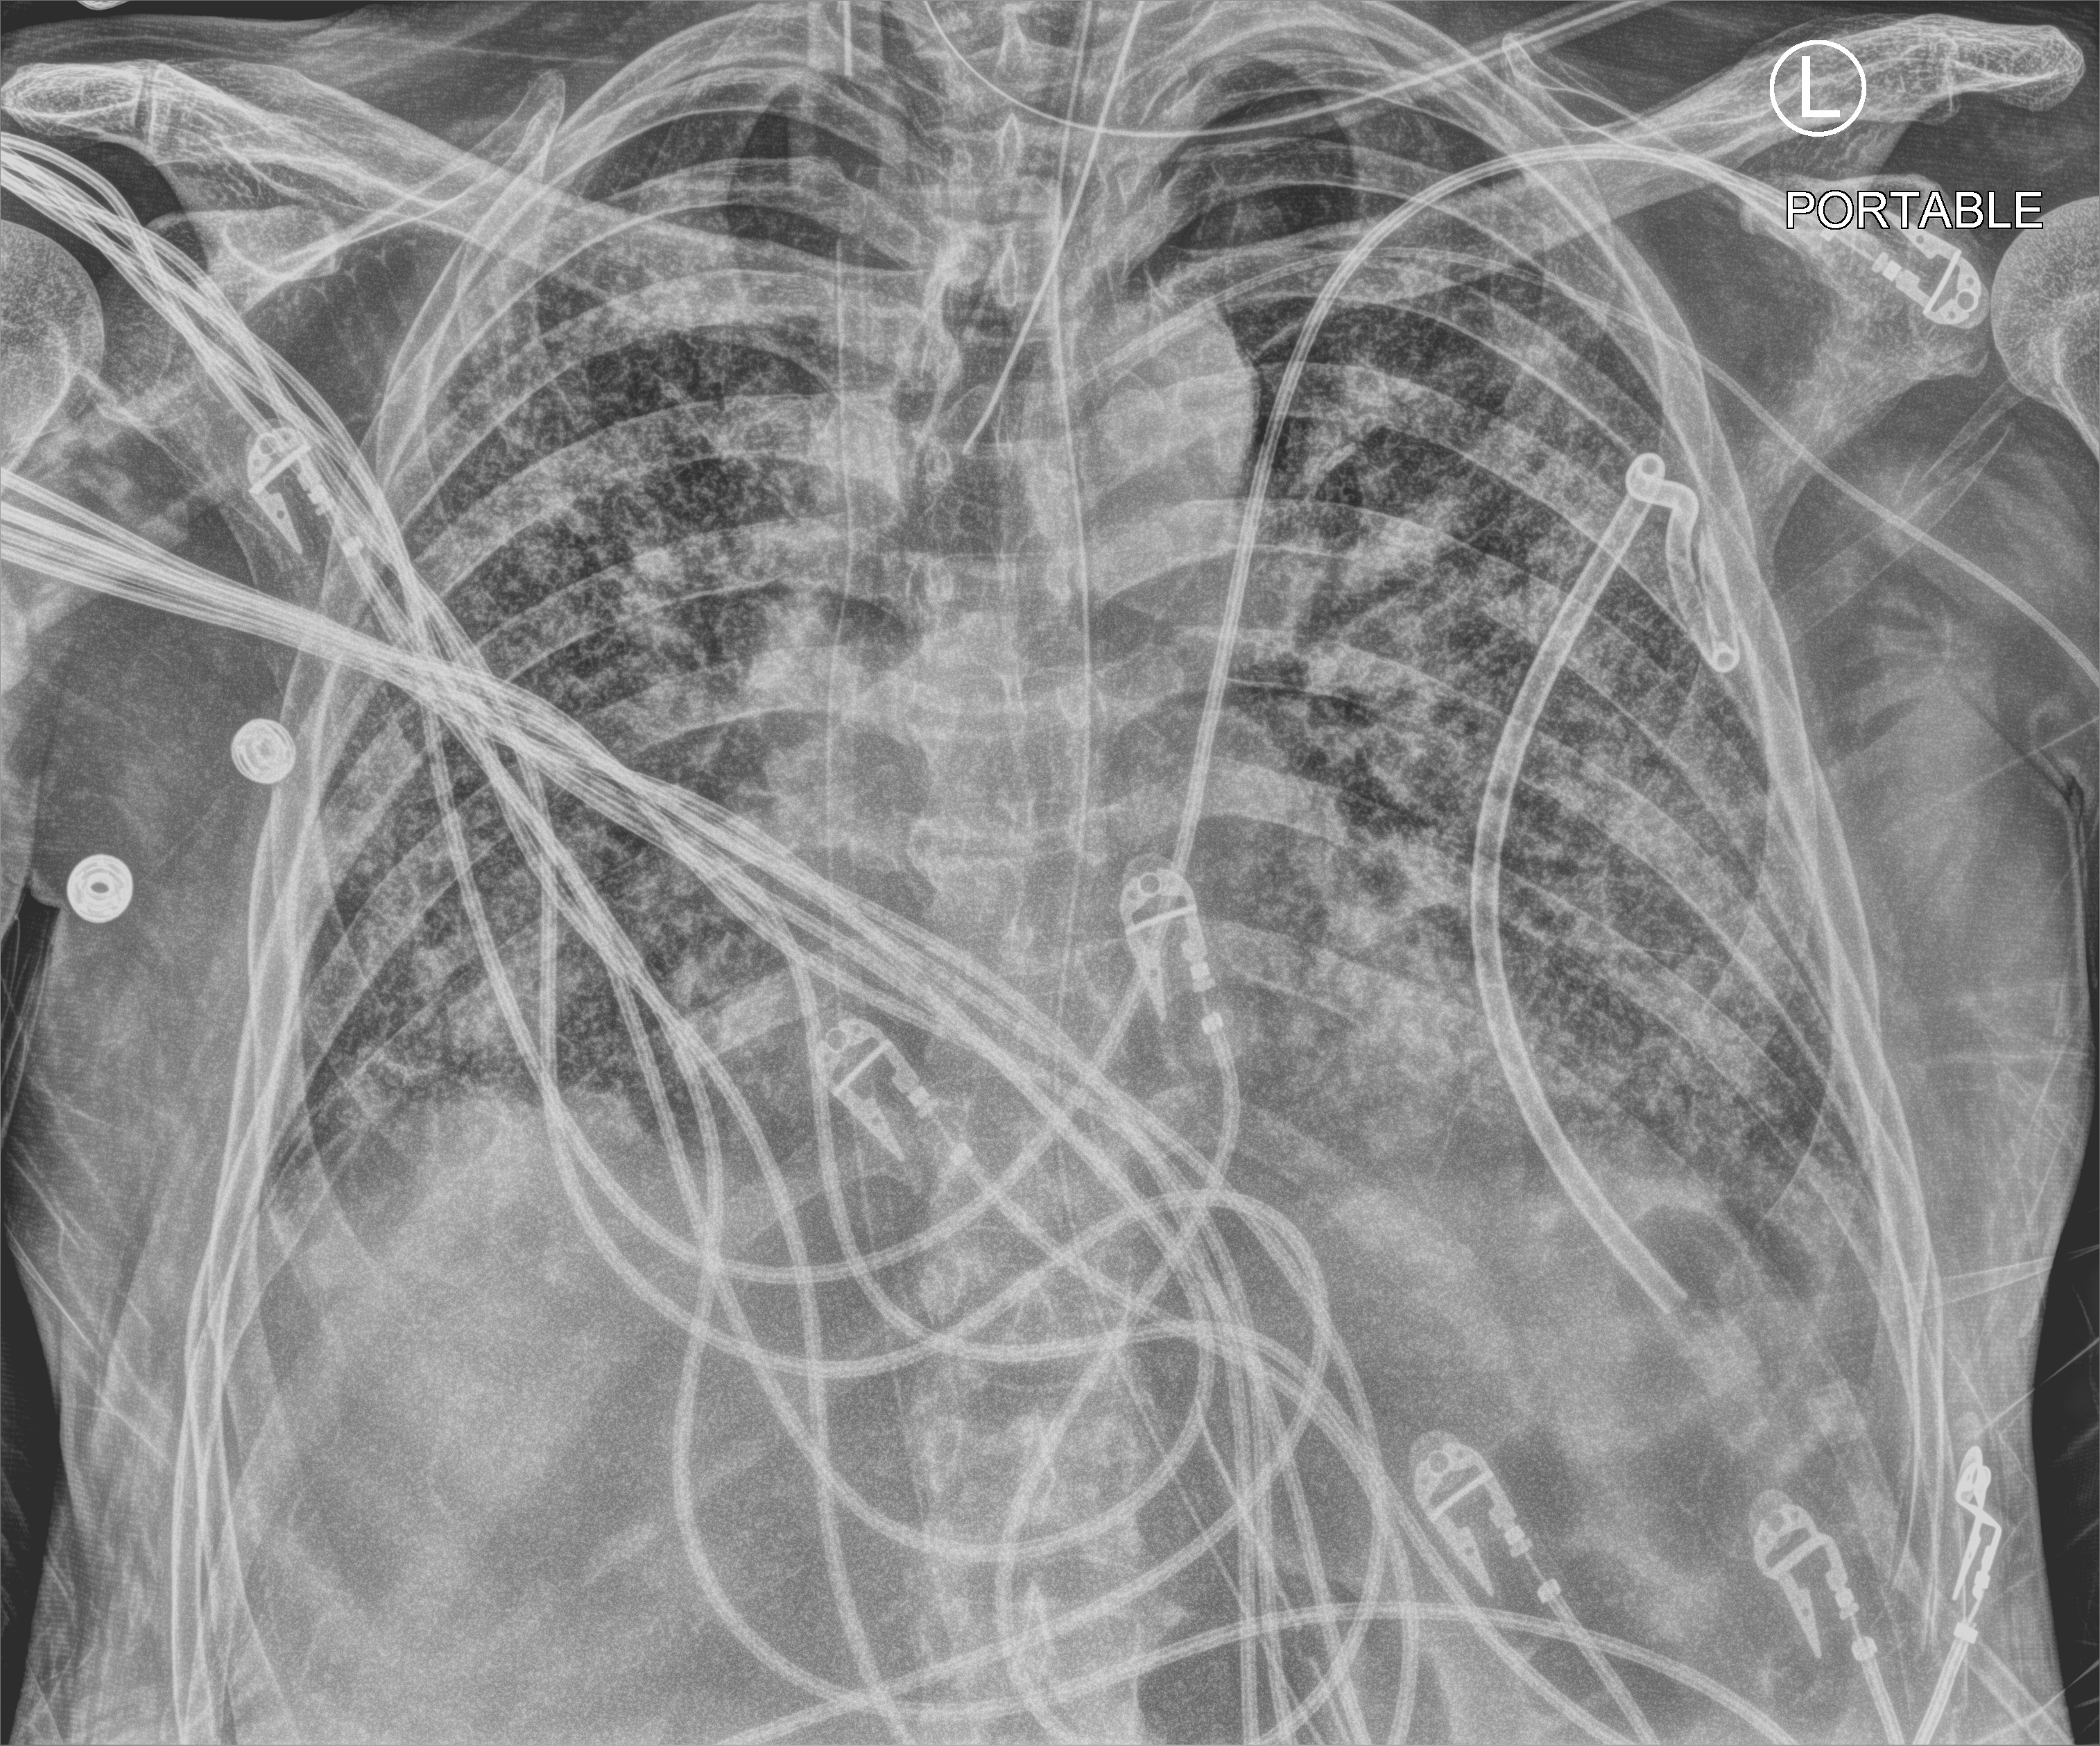
Bedside chest radiograph (computed radiography); anteroposterior (AP) projection. Patient hospitalised with COVID-19; male, aged 60–74 years.
From the hospital-stay record, not from the radiograph (when in the stay this image was taken is not recorded): mechanically ventilated during this hospital stay: yes; admitted to intensive care during this hospital stay: yes.